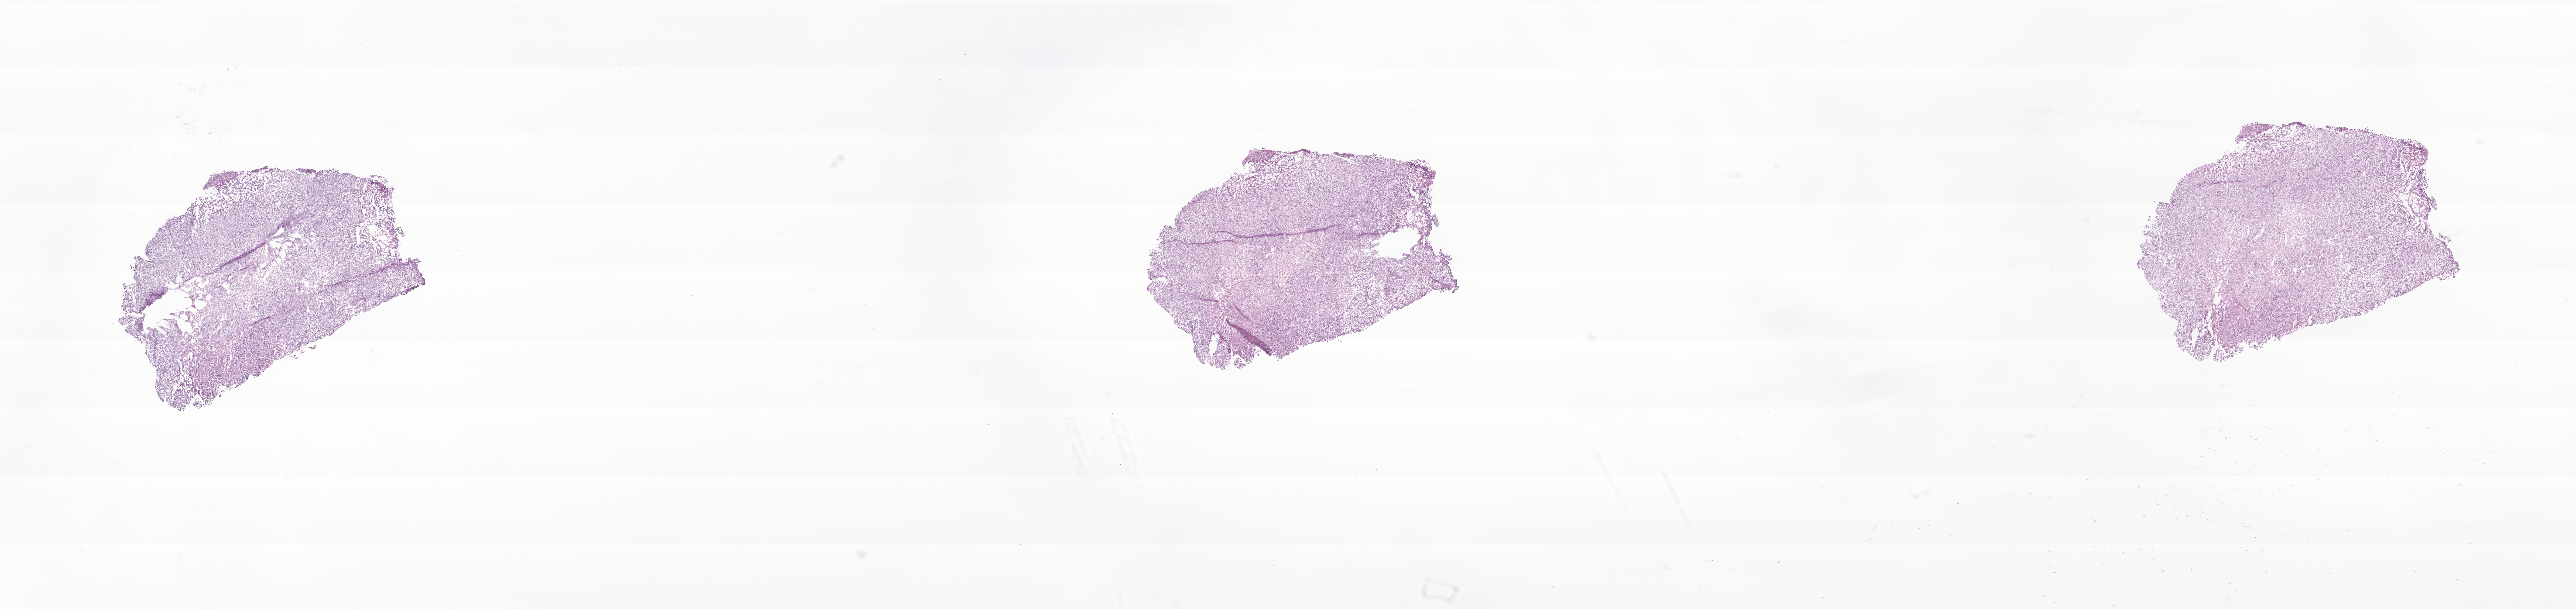
Whole-slide image, H&E stain of tumor tissue from the brain — a low-resolution overview of the entire scanned area, about 40.3 x 9.5 mm. Frozen section (OCT-embedded). Patient female; age 126 months.
Diagnosis: Neoplasm, uncertain whether benign or malignant.